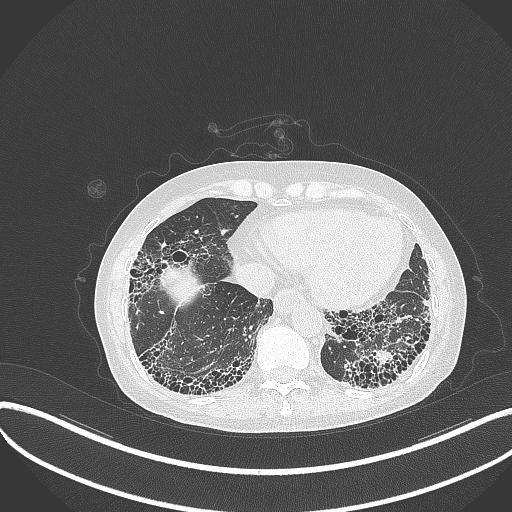
Chest CT, one axial slice. Slice 76 of 373 in the series (ordered by position). 120 kVp. Lung window (W 1500 / L -600 HU). 1 mm slice thickness. 512 × 512 image matrix, field of view 400 × 400 mm. Patient: female, 56 years. From the clinical record (not read from this slice): clinical TNM (as recorded): T1 N0 M0.
Structures marked on this image (rectangle marked by the reading radiologist):
- lung tumour (recorded histology: adenocarcinoma): bounding box (x1, y1, x2, y2) in pixels: (372, 346, 397, 371)